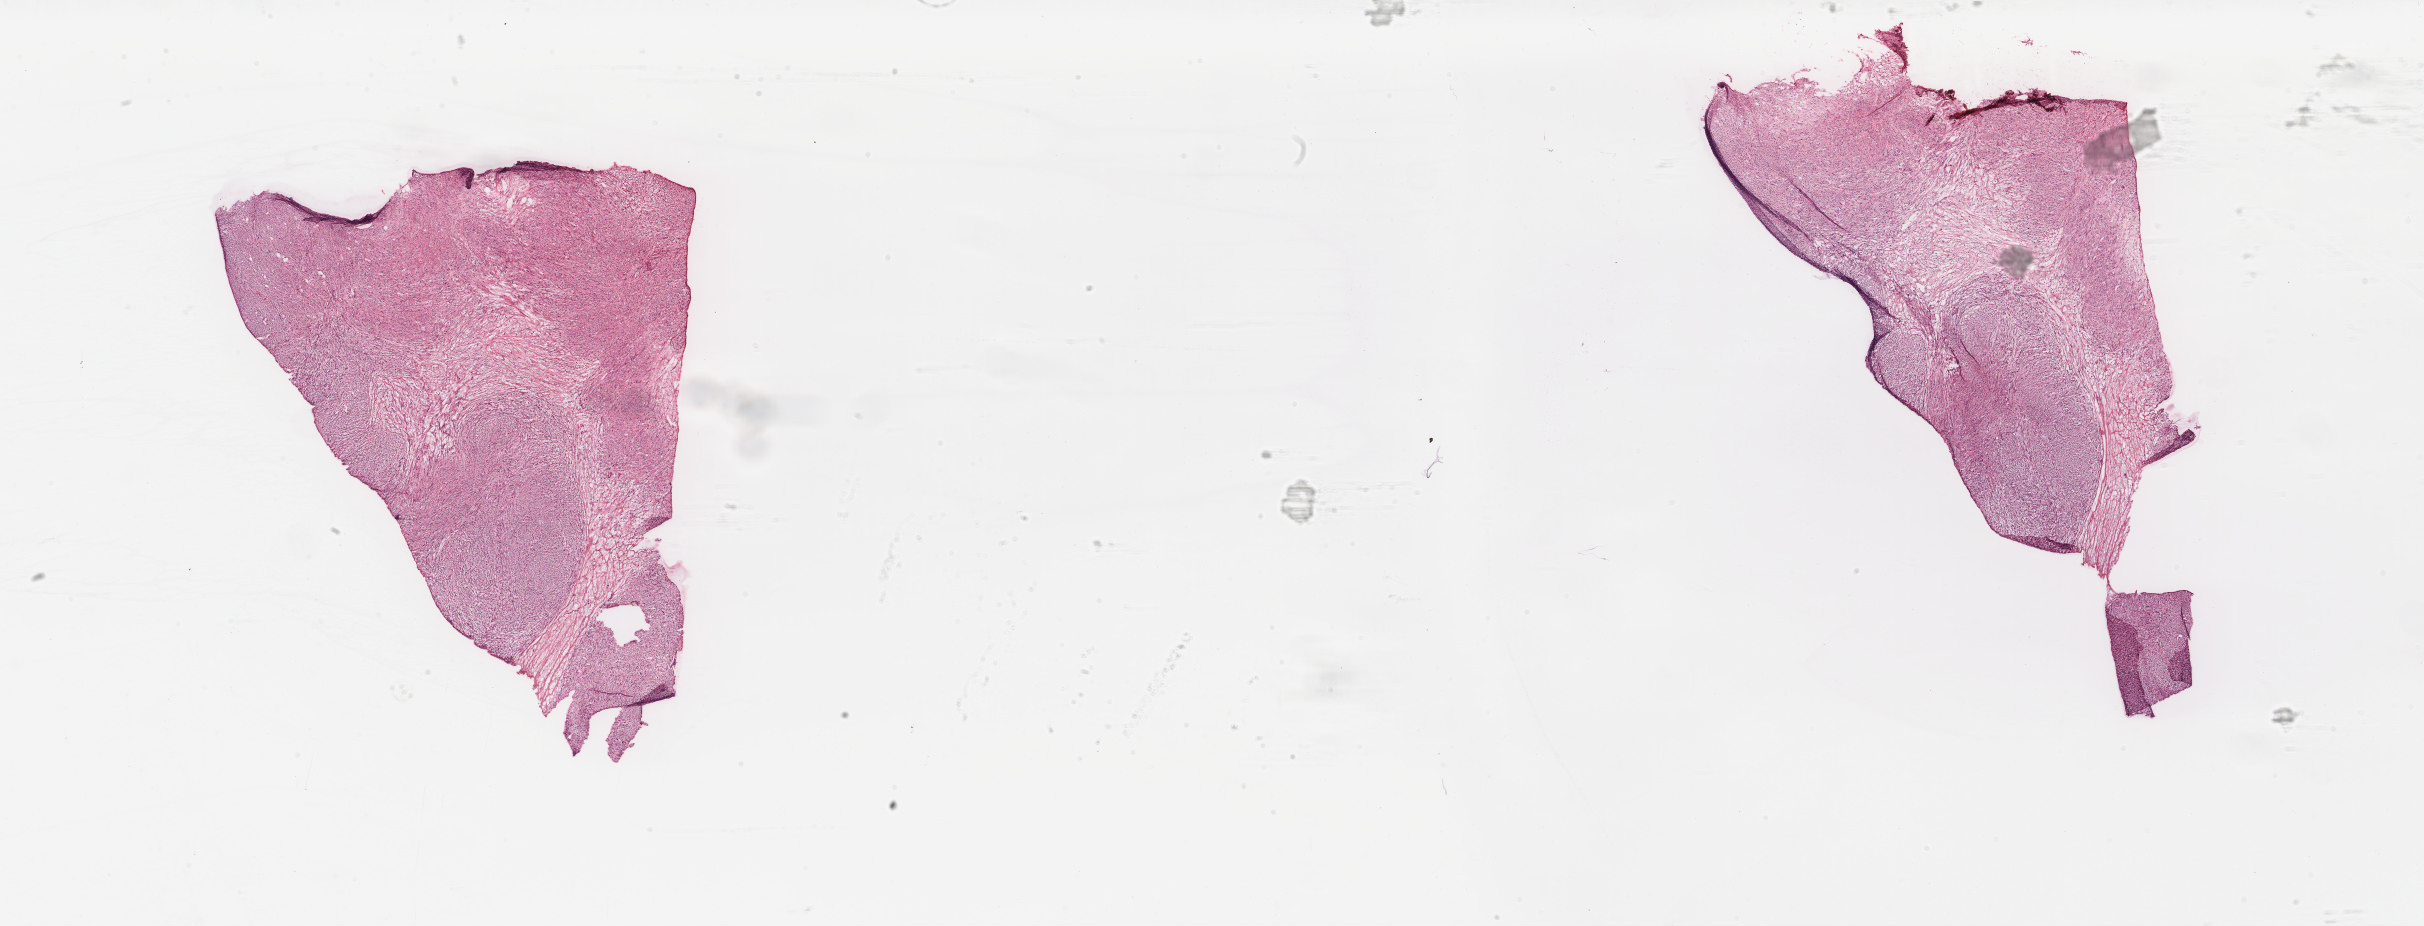
H&E whole-slide image, shown as a low-resolution overview of the whole scanned area (about 38.4 x 14.7 mm, from a 40x scan). Formalin-fixed paraffin-embedded (FFPE) diagnostic section. Primary tumour sample from the retroperitoneum and peritoneum. Patient: female, age at initial diagnosis 58 years.
Pathologic diagnosis: Leiomyosarcoma, NOS (retroperitoneum).